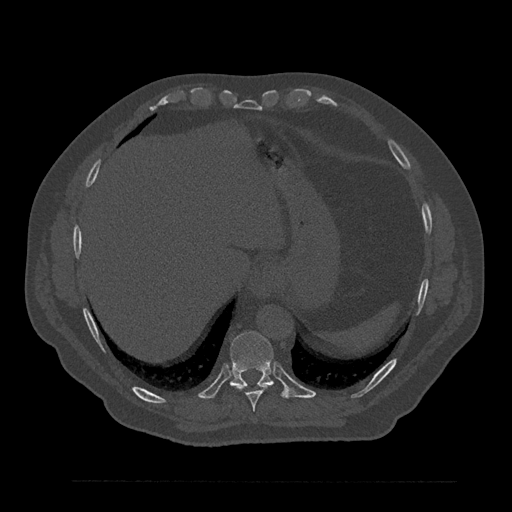
CT including the spine, one axial slice. Position 377 of 797 along the scan axis. Bone window (W 1800 / L 400 HU). 512 × 512 image matrix, field of view 430 × 430 mm. Patient: male, 61 years. From the clinical record (not read from this slice): primary cancer: prostate.
Outlined on this slice (semi-automatic segmentation, software-assisted and operator-edited):
- T10 vertebra: bounding box (x1, y1, x2, y2) in pixels: (229, 331, 286, 397)
- T9 vertebra: (234, 383, 269, 411)